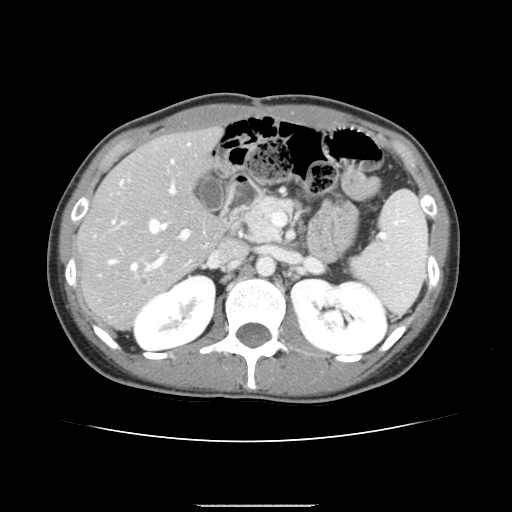
Contrast-enhanced abdominal CT, one axial slice; slice 84 of 150 in the series (ordered by position); 120 kVp; intravenous contrast given; soft-tissue window (W 400 / L 40 HU); 2.5 mm slice thickness; 512 × 512 image matrix, field of view 324 × 324 mm. Female patient, age 32 years. From the clinical record (not read from this slice): diagnosis: colorectal cancer liver metastases, imaged before liver resection; multiple liver metastases: yes; largest metastasis: 0.7 cm; chemotherapy before resection: yes.
Outlined on this slice (expert manual segmentation):
- hepatic veins: bounding box [x1, y1, x2, y2] px = [109, 144, 189, 269]
- liver: [78, 130, 225, 327]
- planned liver remnant (the part of the liver to remain after resection): [78, 129, 225, 276]
- portal vein (with intrahepatic branches): [109, 182, 189, 271]
- liver metastasis: [142, 280, 149, 286]